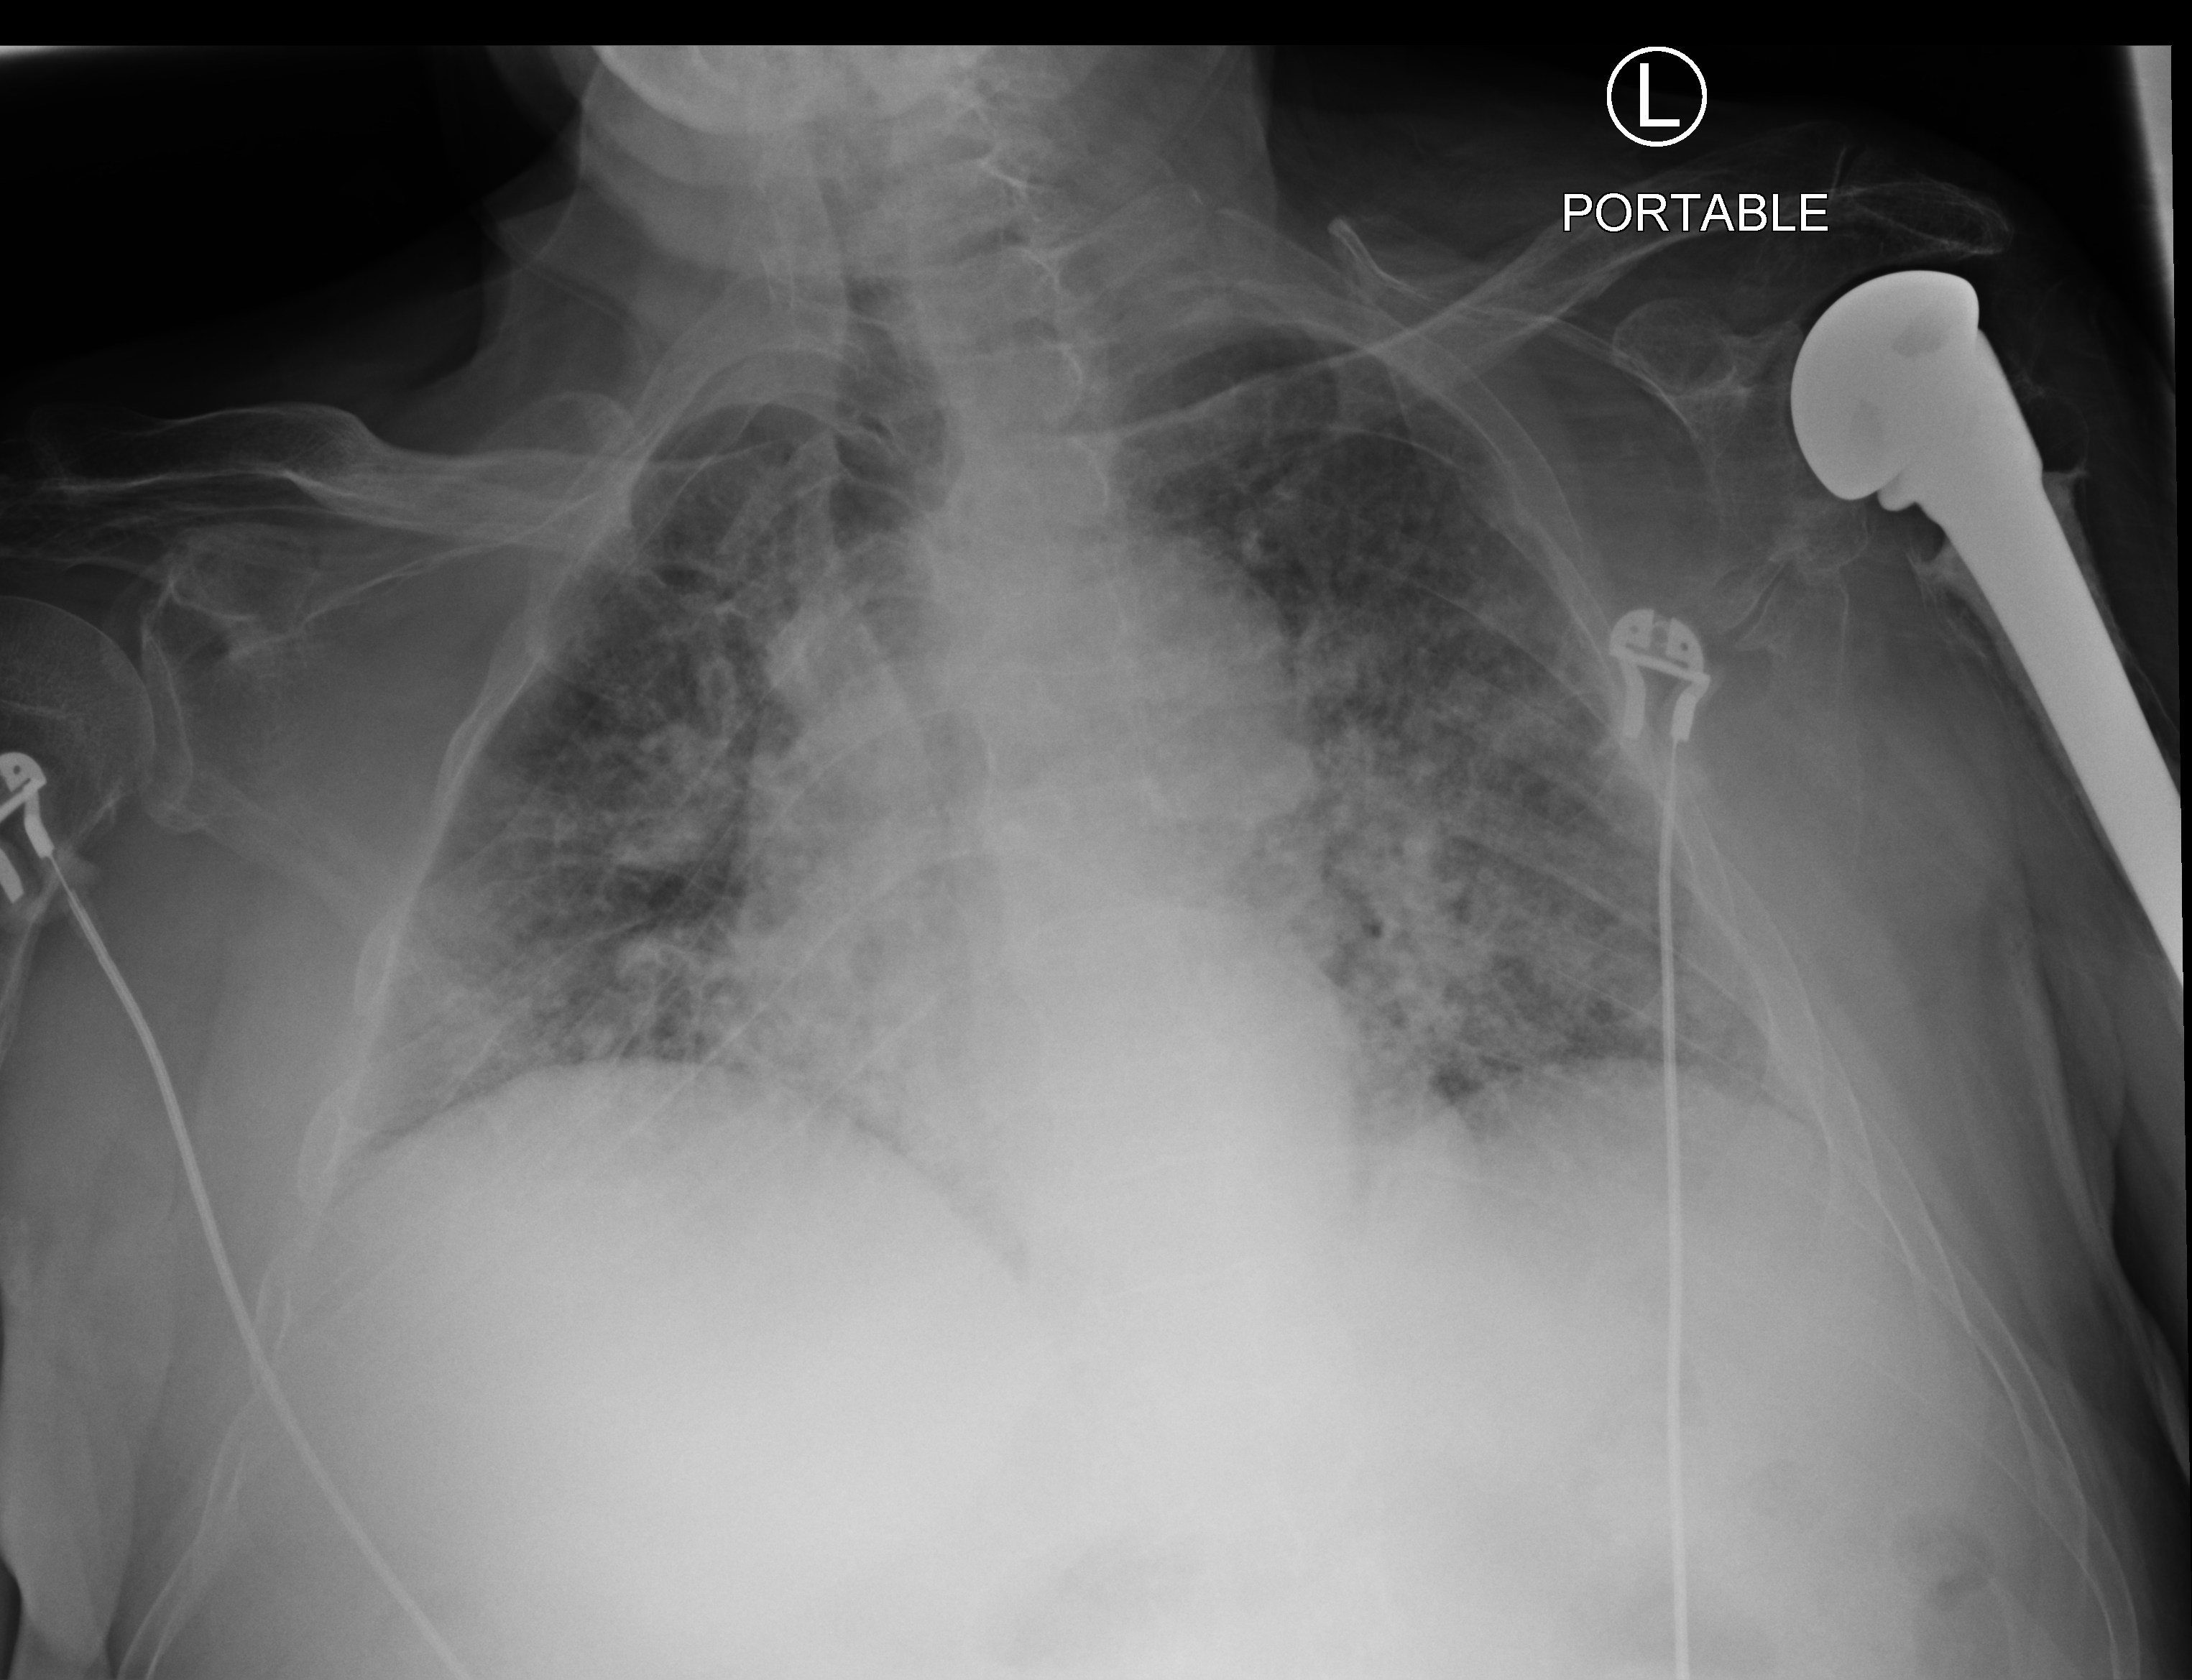
Bedside chest radiograph (computed radiography), anteroposterior (AP) projection. Patient hospitalised with COVID-19; male, aged 60–74 years.
From the hospital-stay record, not from the radiograph (when in the stay this image was taken is not recorded): diabetes (admission record): no.